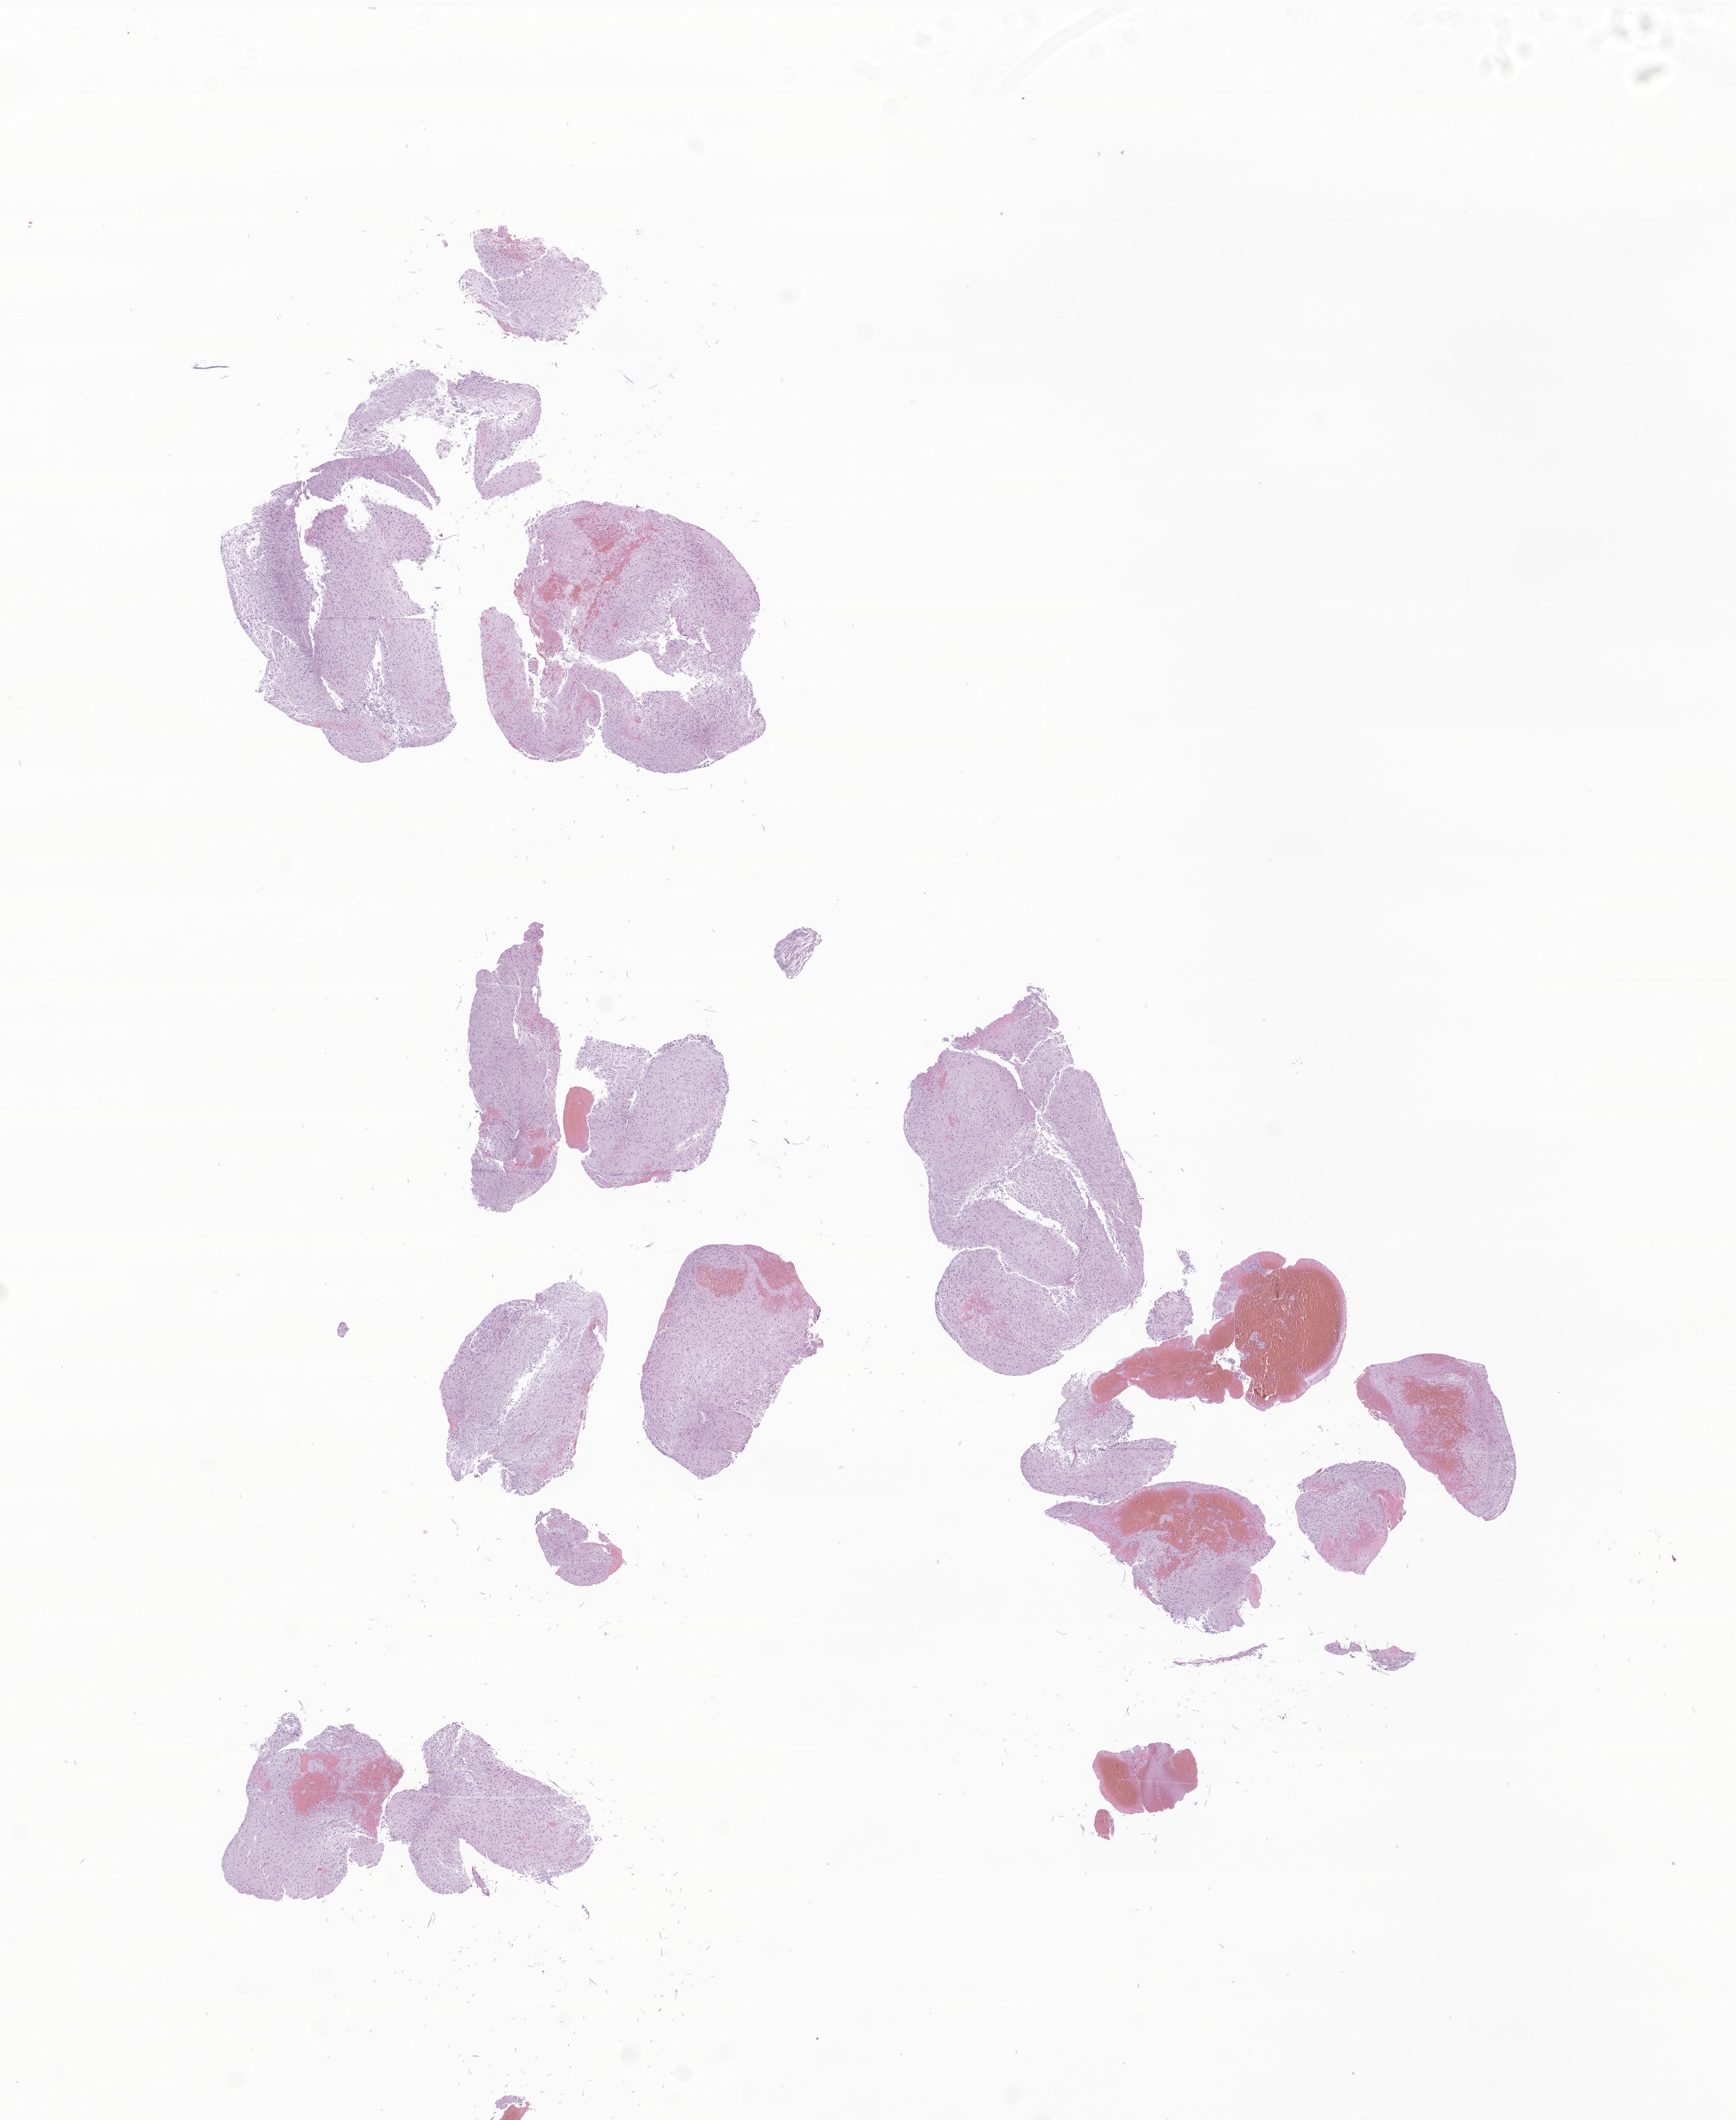
Hematoxylin and eosin (H&E) whole-slide image of tumor tissue from the cerebrum, low-resolution overview of the scanned area, about 14.6 x 17.8 mm; FFPE section. Patient female; age 123 months (10 years 3 months).
Recorded diagnosis: Pilocytic astrocytoma.